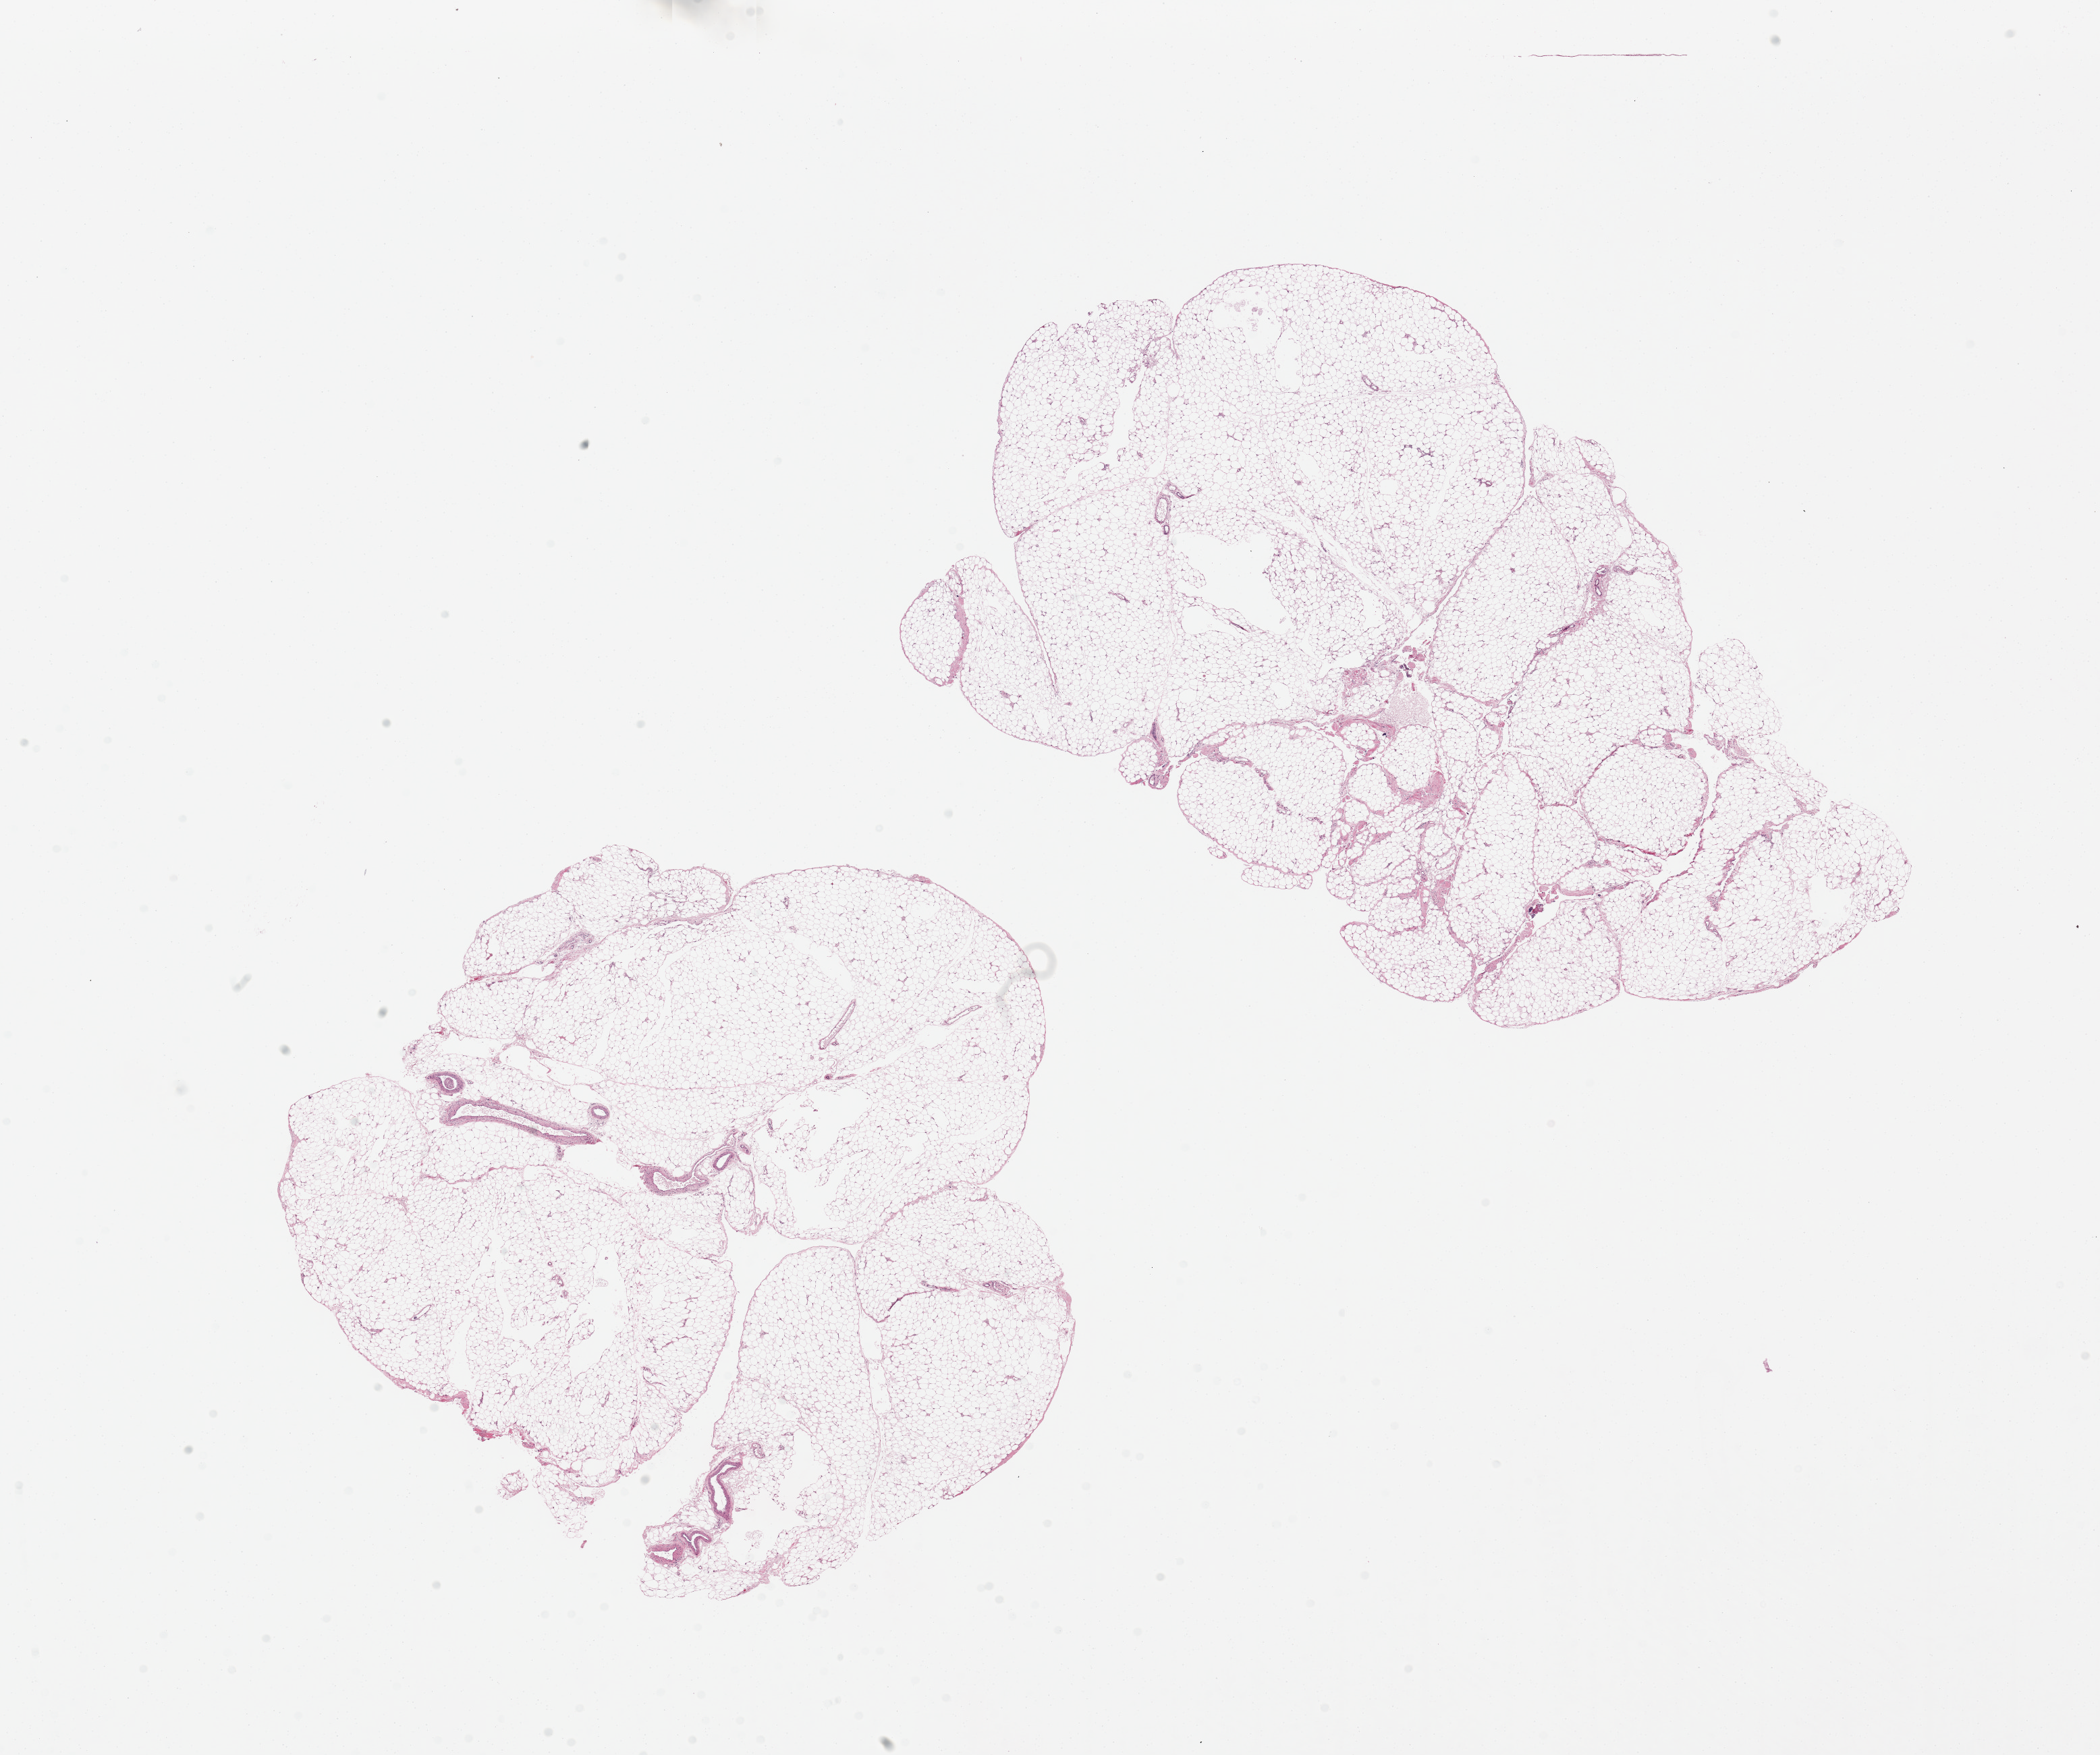
Whole-slide image, haematoxylin and eosin stain, brightfield — whole scanned area (about 24.6 x 20.6 mm, acquisition: 20x scan) shown as a low-resolution overview, PAXgene-fixed paraffin-embedded (PFPE) section, sampled site (target tissue): omentum, tissue donor sample. Male donor.
* review note (as recorded): 2 pieces, 9x9 & 12x7mm